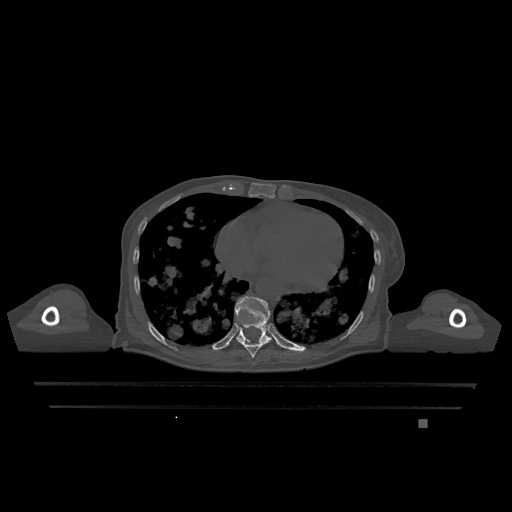
CT including the spine, one axial slice. Slice 670 of 1317 in the series (ordered by position). Bone window (W 1800 / L 400 HU). 0.5 mm slice thickness. 512 × 512 image matrix, field of view 500 × 500 mm. Female patient, age 74 years. Case-level facts recorded for this patient, not image findings: primary cancer: lung.
Structures marked on this image (semi-automatic segmentation, software-assisted and operator-edited):
- T10 vertebra: bounding box [x1, y1, x2, y2] px = [235, 296, 271, 342]
- T9 vertebra: [236, 339, 271, 358]